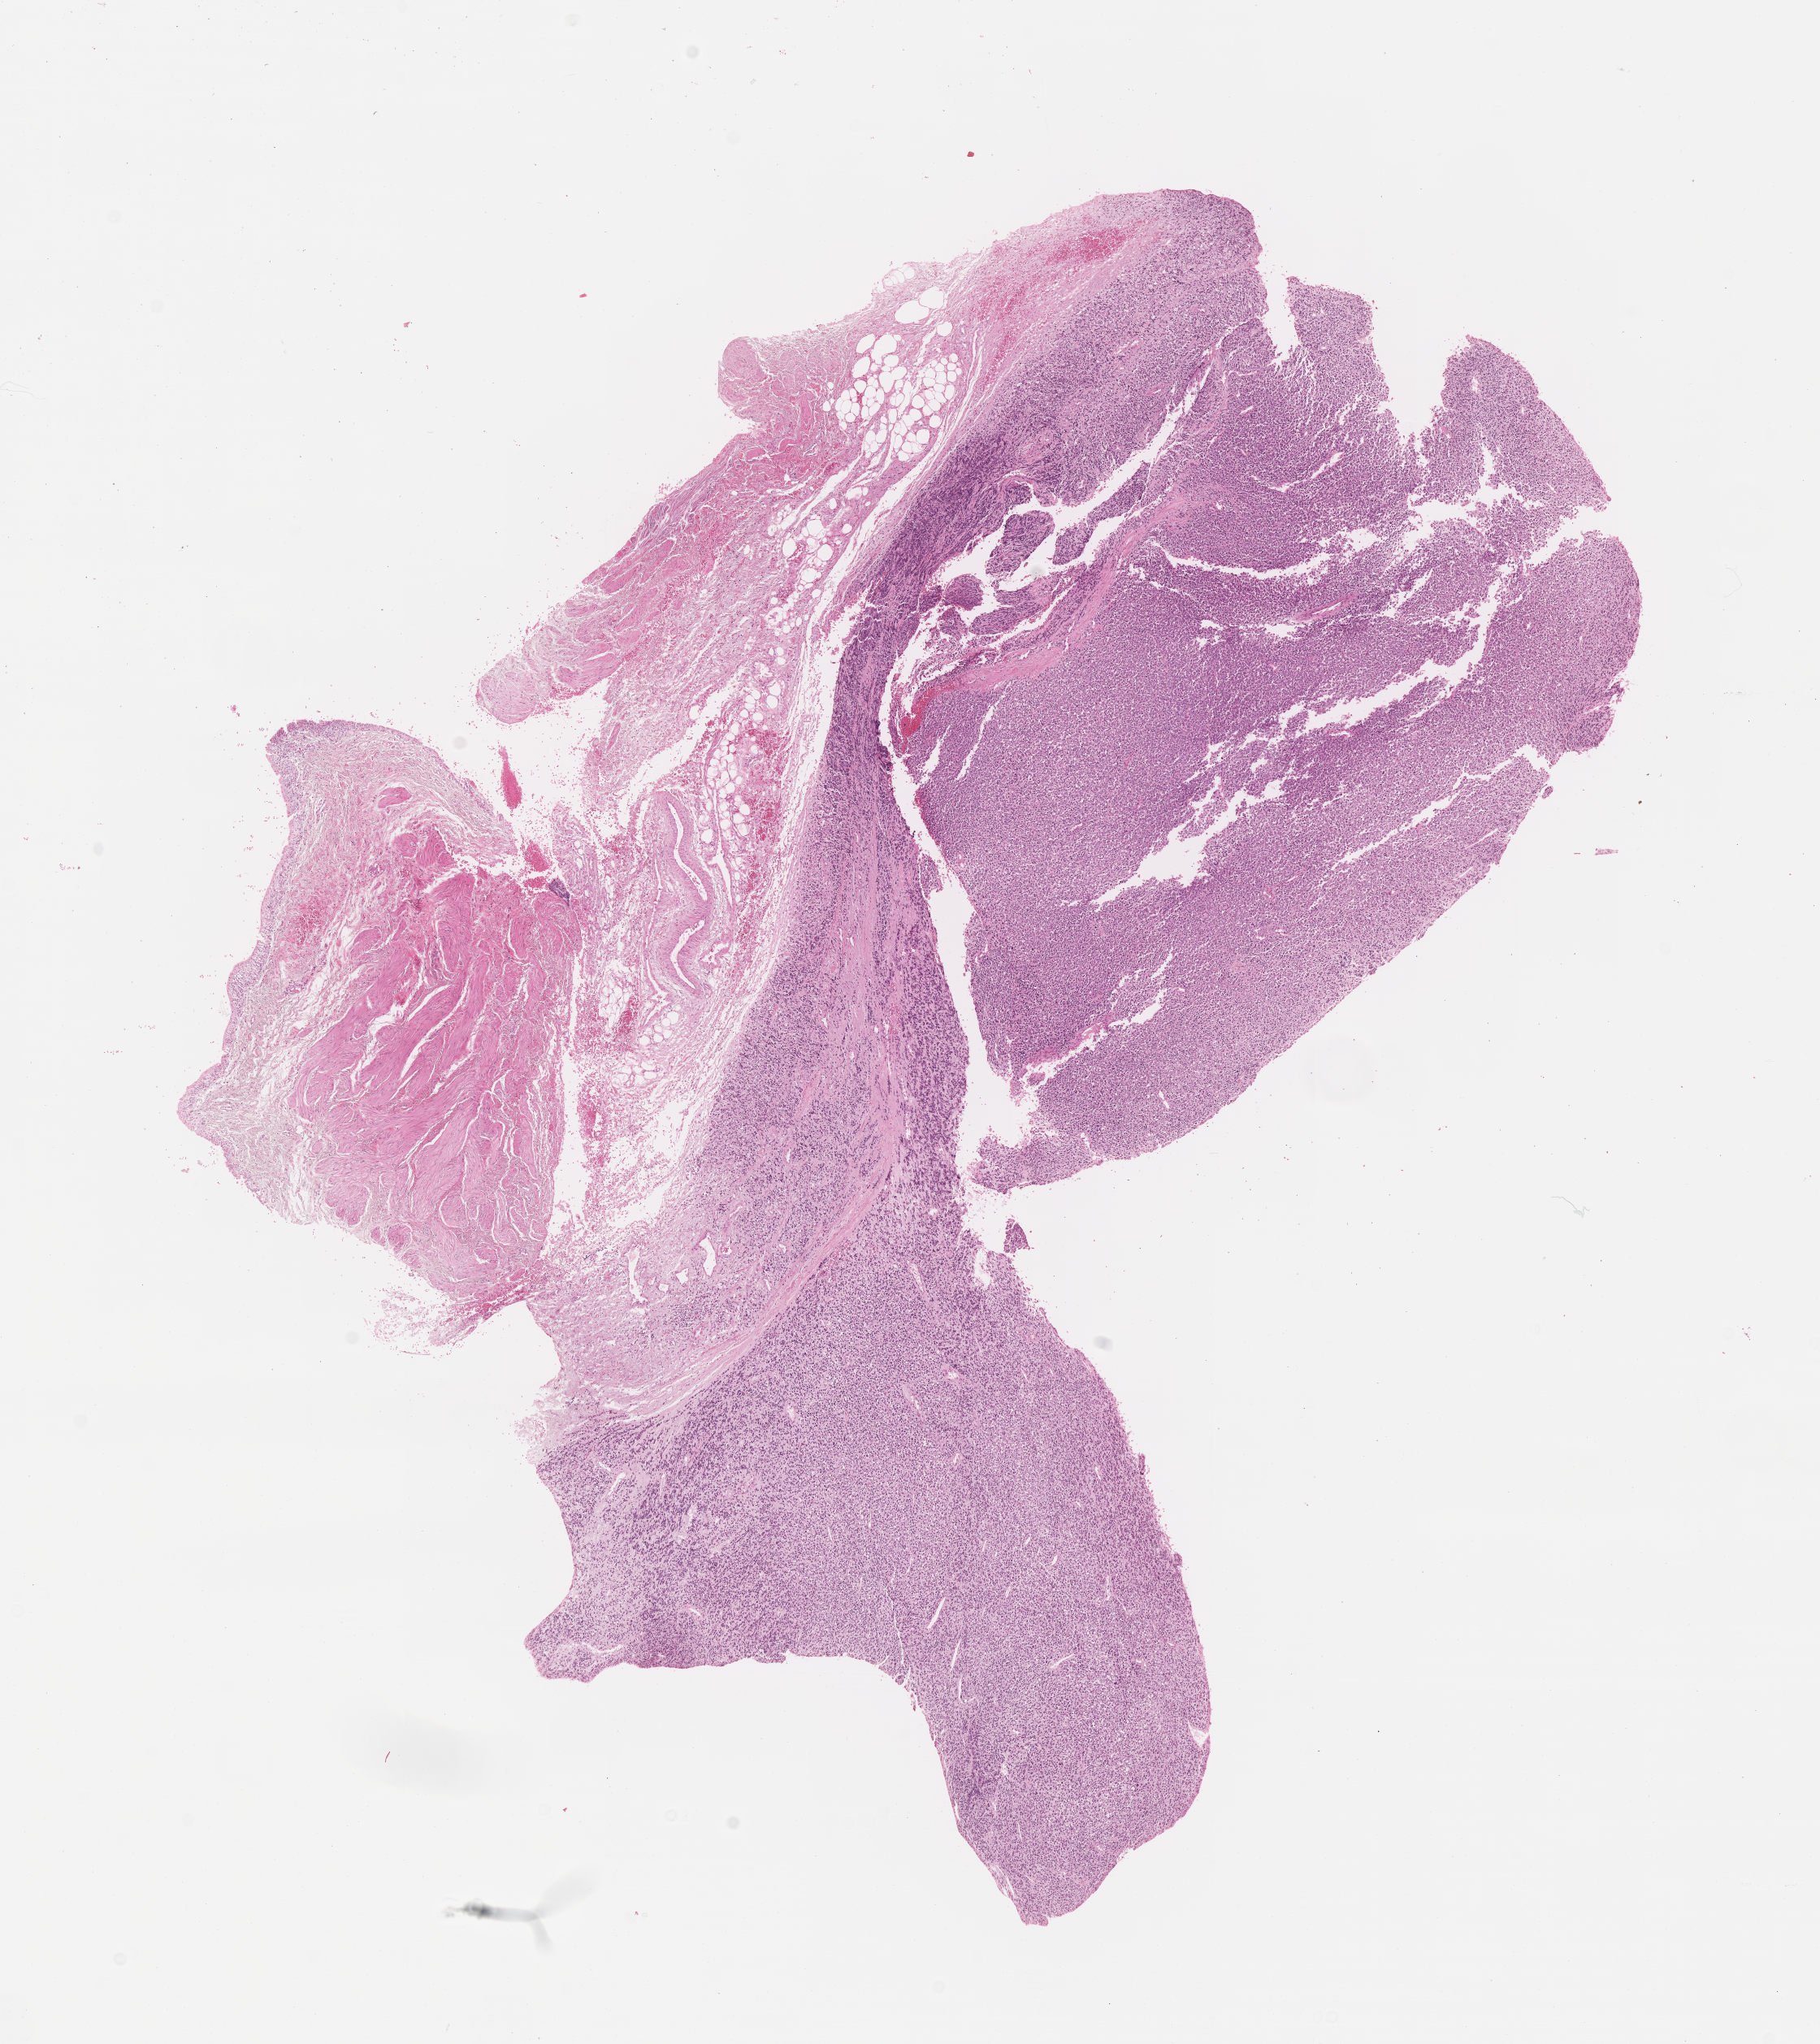
Digitized hematoxylin and eosin (H&E)-stained section of tumor tissue, a low-resolution overview of the entire scanned area, about 9.1 x 10.2 mm, FFPE section, sample anatomic site: pelvis. Patient: female, age 9.0 years at diagnosis.
Diagnosis: rhabdomyosarcoma; histological classification: embryonal rhabdomyosarcoma. Metastatic status at presentation (as recorded): non-metastatic (unconfirmed).